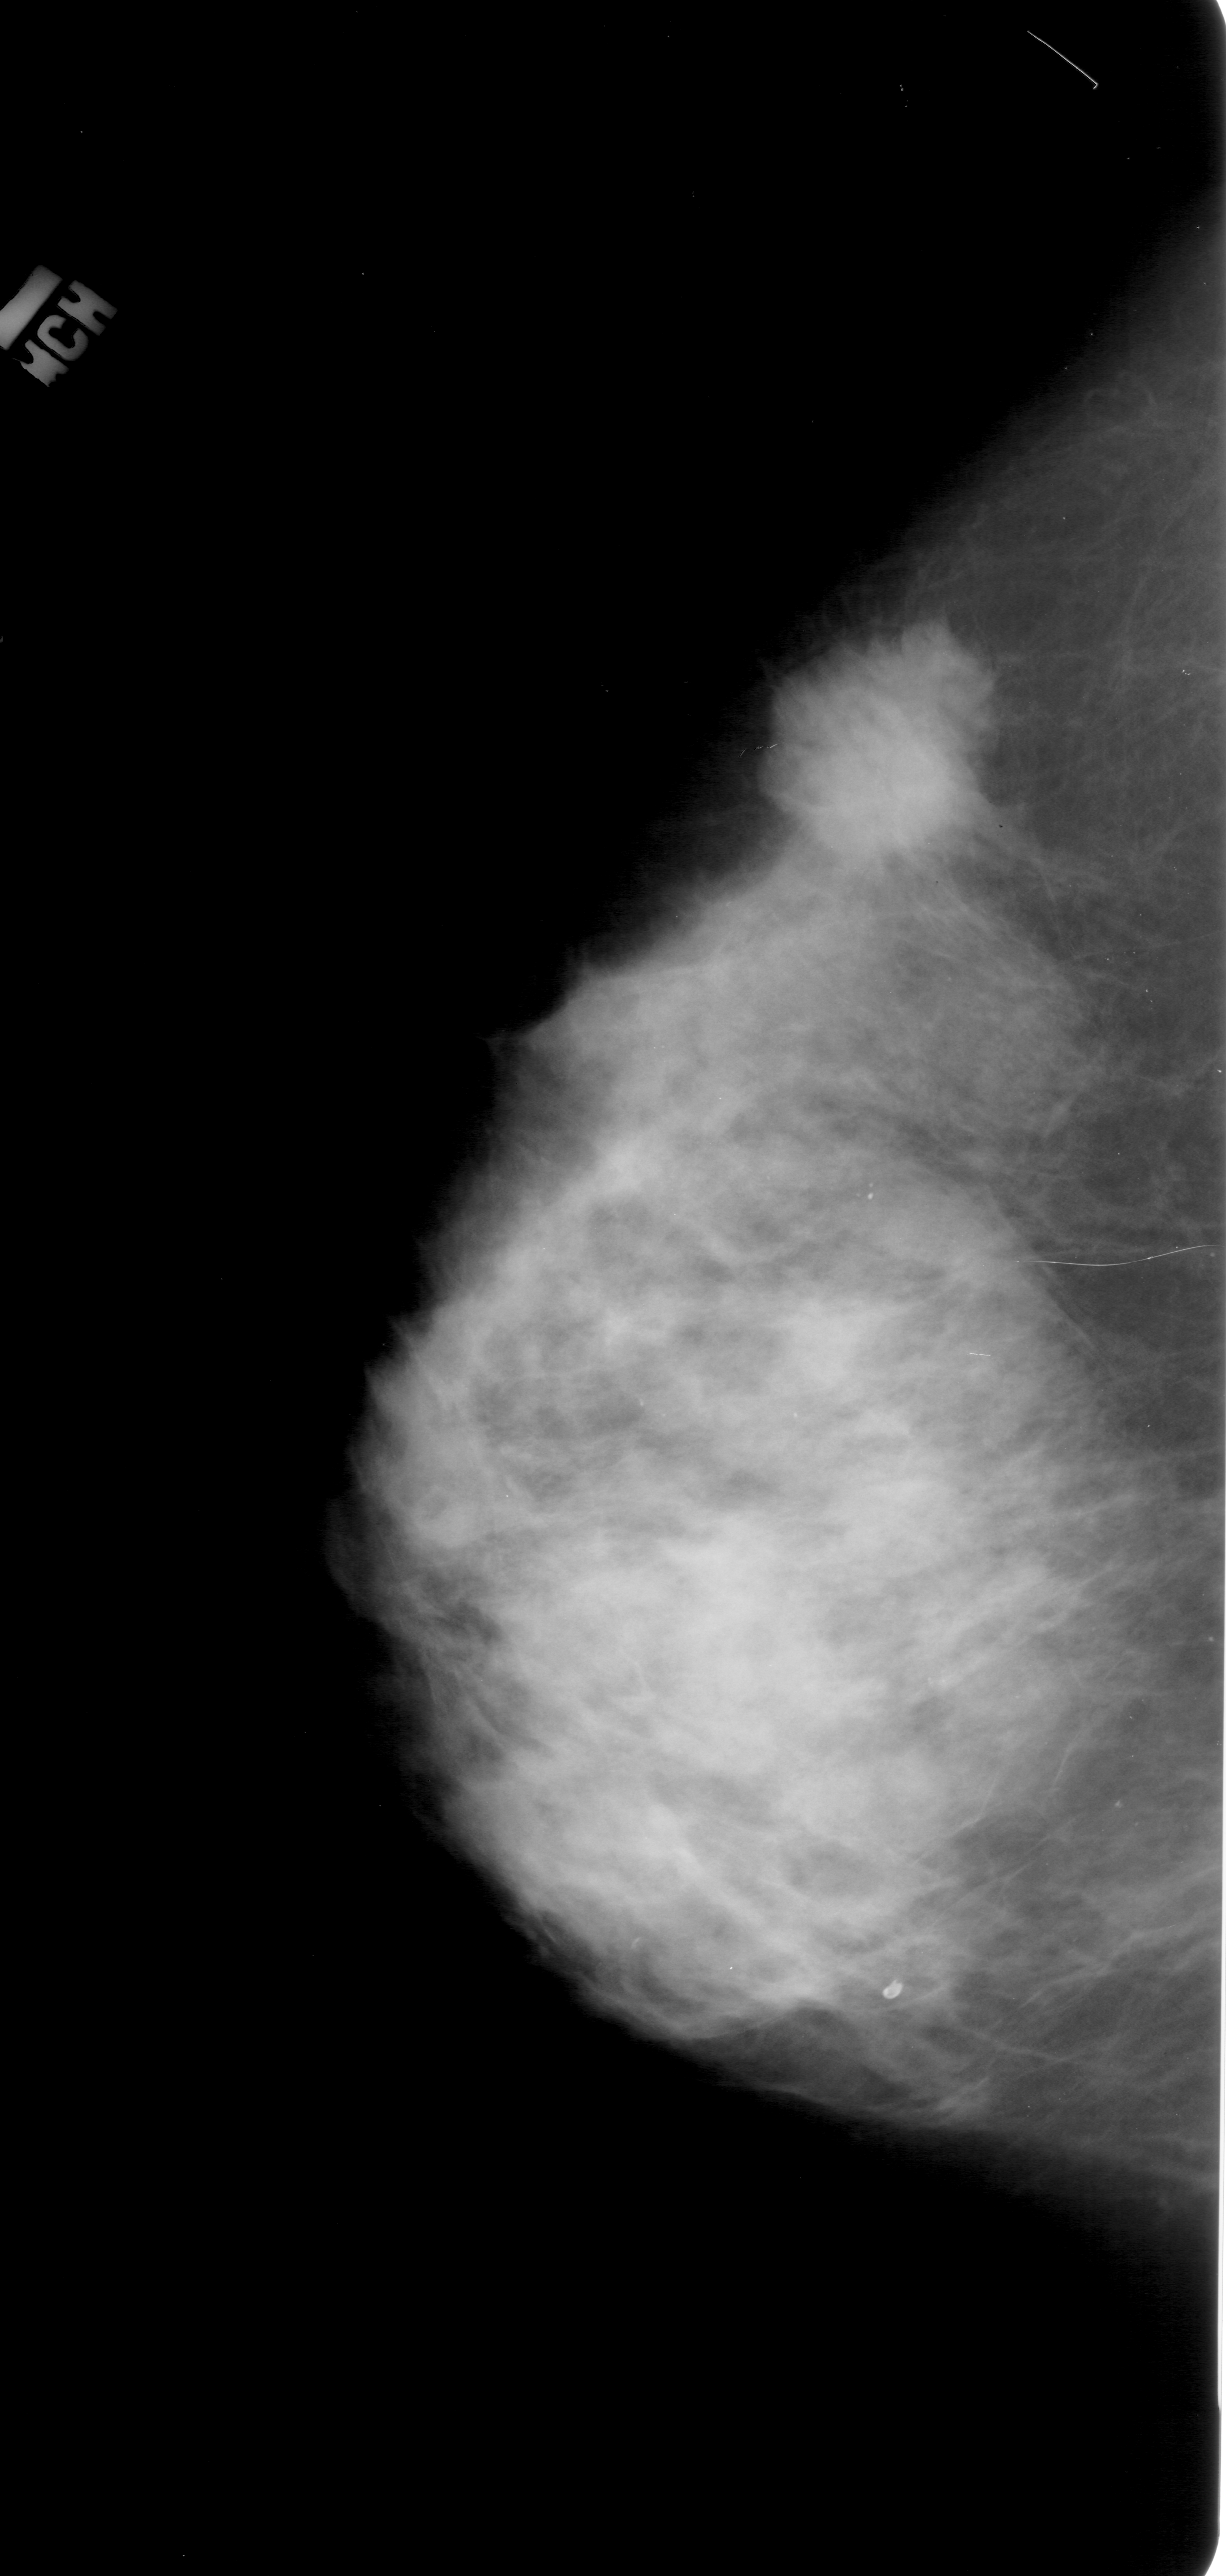
Mammogram (digitized film); left breast; craniocaudal (CC) view; BI-RADS breast density category 4 (scale 1–4); 1226 × 2576 image matrix.
Expert-marked regions of interest on this film, with their recorded descriptors:
- mass, shape irregular, margins spiculated; BI-RADS assessment category 5; pathology (as recorded): malignant: bounding box (x1, y1, x2, y2) in pixels: (759, 654, 981, 838)